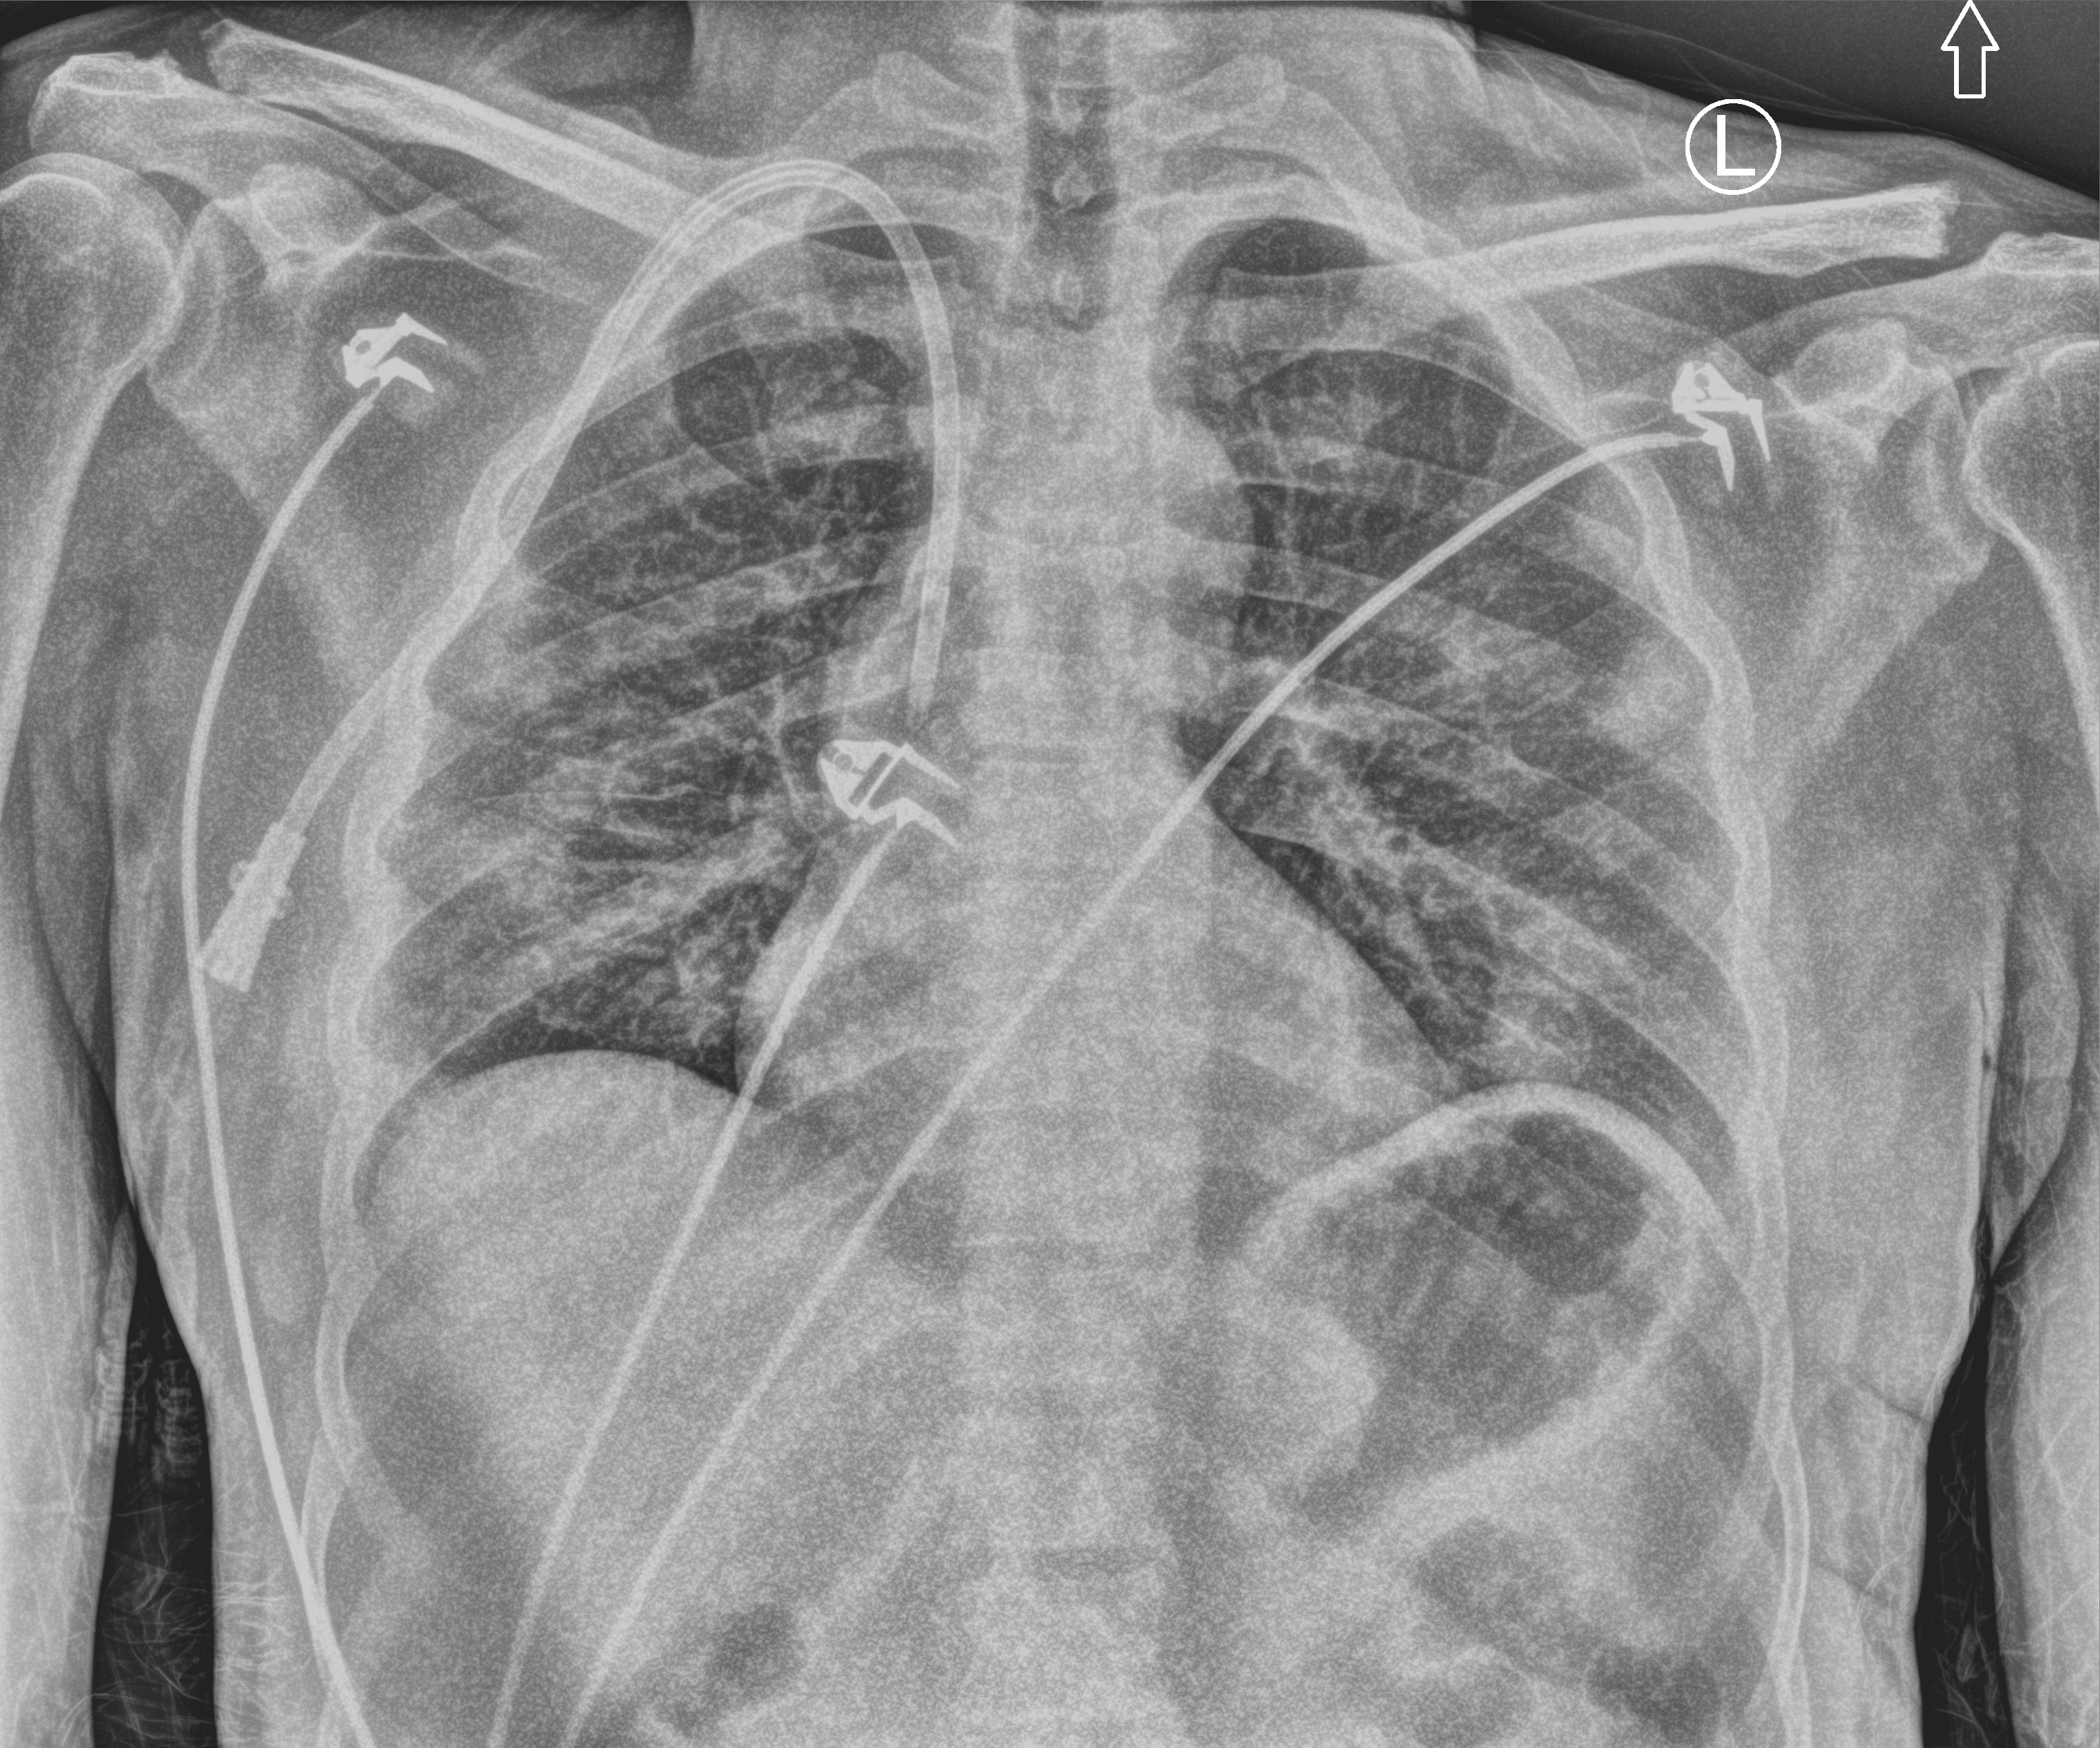
Chest X-ray (portable). Male patient hospitalised with COVID-19, age 18–59 years.
Hospital-stay facts (about this admission, not read from this image; timing relative to this image not recorded): diabetes (admission record): no; mechanically ventilated during this hospital stay: no.